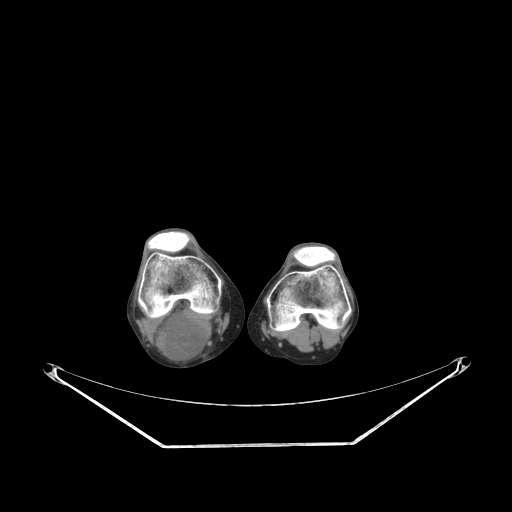
CT of an extremity soft-tissue mass (from a PET/CT study), one axial slice. Position 168 of 267 along the scan axis. Reconstruction kernel SOFT. 140 kVp. Soft-tissue window (W 400 / L 40 HU). 3.75 mm slice thickness. 512 × 512 image matrix, field of view 500 × 500 mm. Female patient. From the clinical record (not read from this slice): histological type: liposarcoma; site of the primary tumour: right thigh.
Annotated regions visible in this slice (expert contour drawn on MRI and transferred to this co-registered scan by the dataset authors):
- gross tumour volume (mass): box from (x=153, y=313) to (x=207, y=359) px